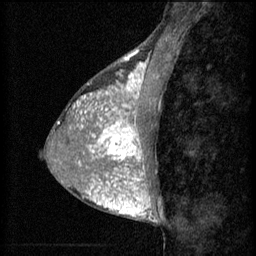
Breast MRI (dynamic contrast-enhanced), one sagittal slice. Position 27 of 60 along the scan axis. 3 images stored at this slice position (order not interpretable as contrast timing). 1.5 T. TE 4.2 ms, TR 8.2 ms. 2 mm slice thickness. 256 × 256 image matrix. Female patient, age 38 years.
Annotated regions visible in this slice (semi-automatically segmented with operator editing):
- analysis volume of interest (the breast-tissue region the enhancement analysis was run in; not a lesion): bounding box <95,106,156,171> (left, top, right, bottom; pixels)
- tumour enhancement mask (voxels above the 70 % enhancement threshold inside the analysis volume of interest): <95,106,145,171>